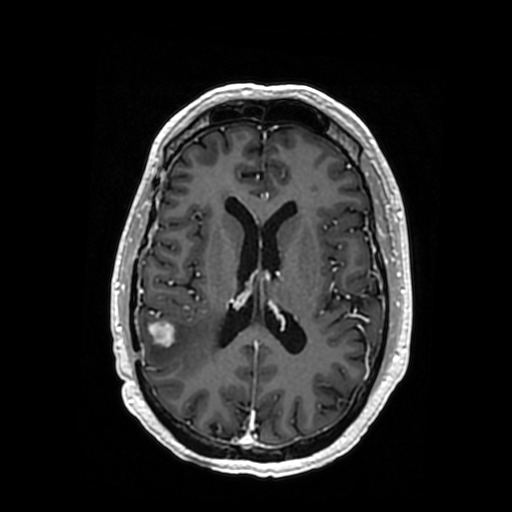
Brain MRI from a brain-tumour surgery series, one axial slice; slice 161 of 364 in the series (ordered by position); T1-weighted post-contrast; 512 × 512 image matrix, field of view 260 × 260 mm. From the clinical record (not read from this slice): histopathology: Oligodendroglioma; WHO grade: 3; IDH mutation: yes; tumour location: Right Posterior Temporal Inferior Parietal.
Annotated regions visible in this slice (expert manual segmentation):
- tumour: bounding box <146,320,217,346> (left, top, right, bottom; pixels)